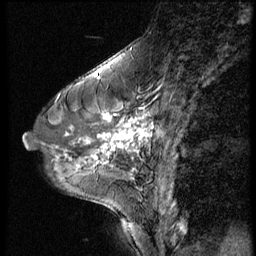
Breast MRI (dynamic contrast-enhanced), one sagittal slice. Slice 22 of 56 in the series (ordered by position). Dynamic contrast-enhanced series, image 2 of 3 at this slice position (ordered by acquisition). 1.5 T. TE 4.2 ms, TR 9 ms. 2.5 mm slice thickness. 256 × 256 image matrix, field of view 180 × 180 mm. Patient: female, 46 years. Case-level facts recorded for this patient, not image findings: setting: breast cancer imaged before/during neoadjuvant chemotherapy; receptor status: HER2-positive.
Outlined on this slice (semi-automatic segmentation, software-assisted and operator-edited):
- analysis volume of interest (the breast-tissue region the enhancement analysis was run in; not a lesion): box from (x=64, y=98) to (x=174, y=182) px
- tumour enhancement mask (voxels above the 140 % enhancement threshold inside the analysis volume of interest): (x=93, y=113)–(x=155, y=162)